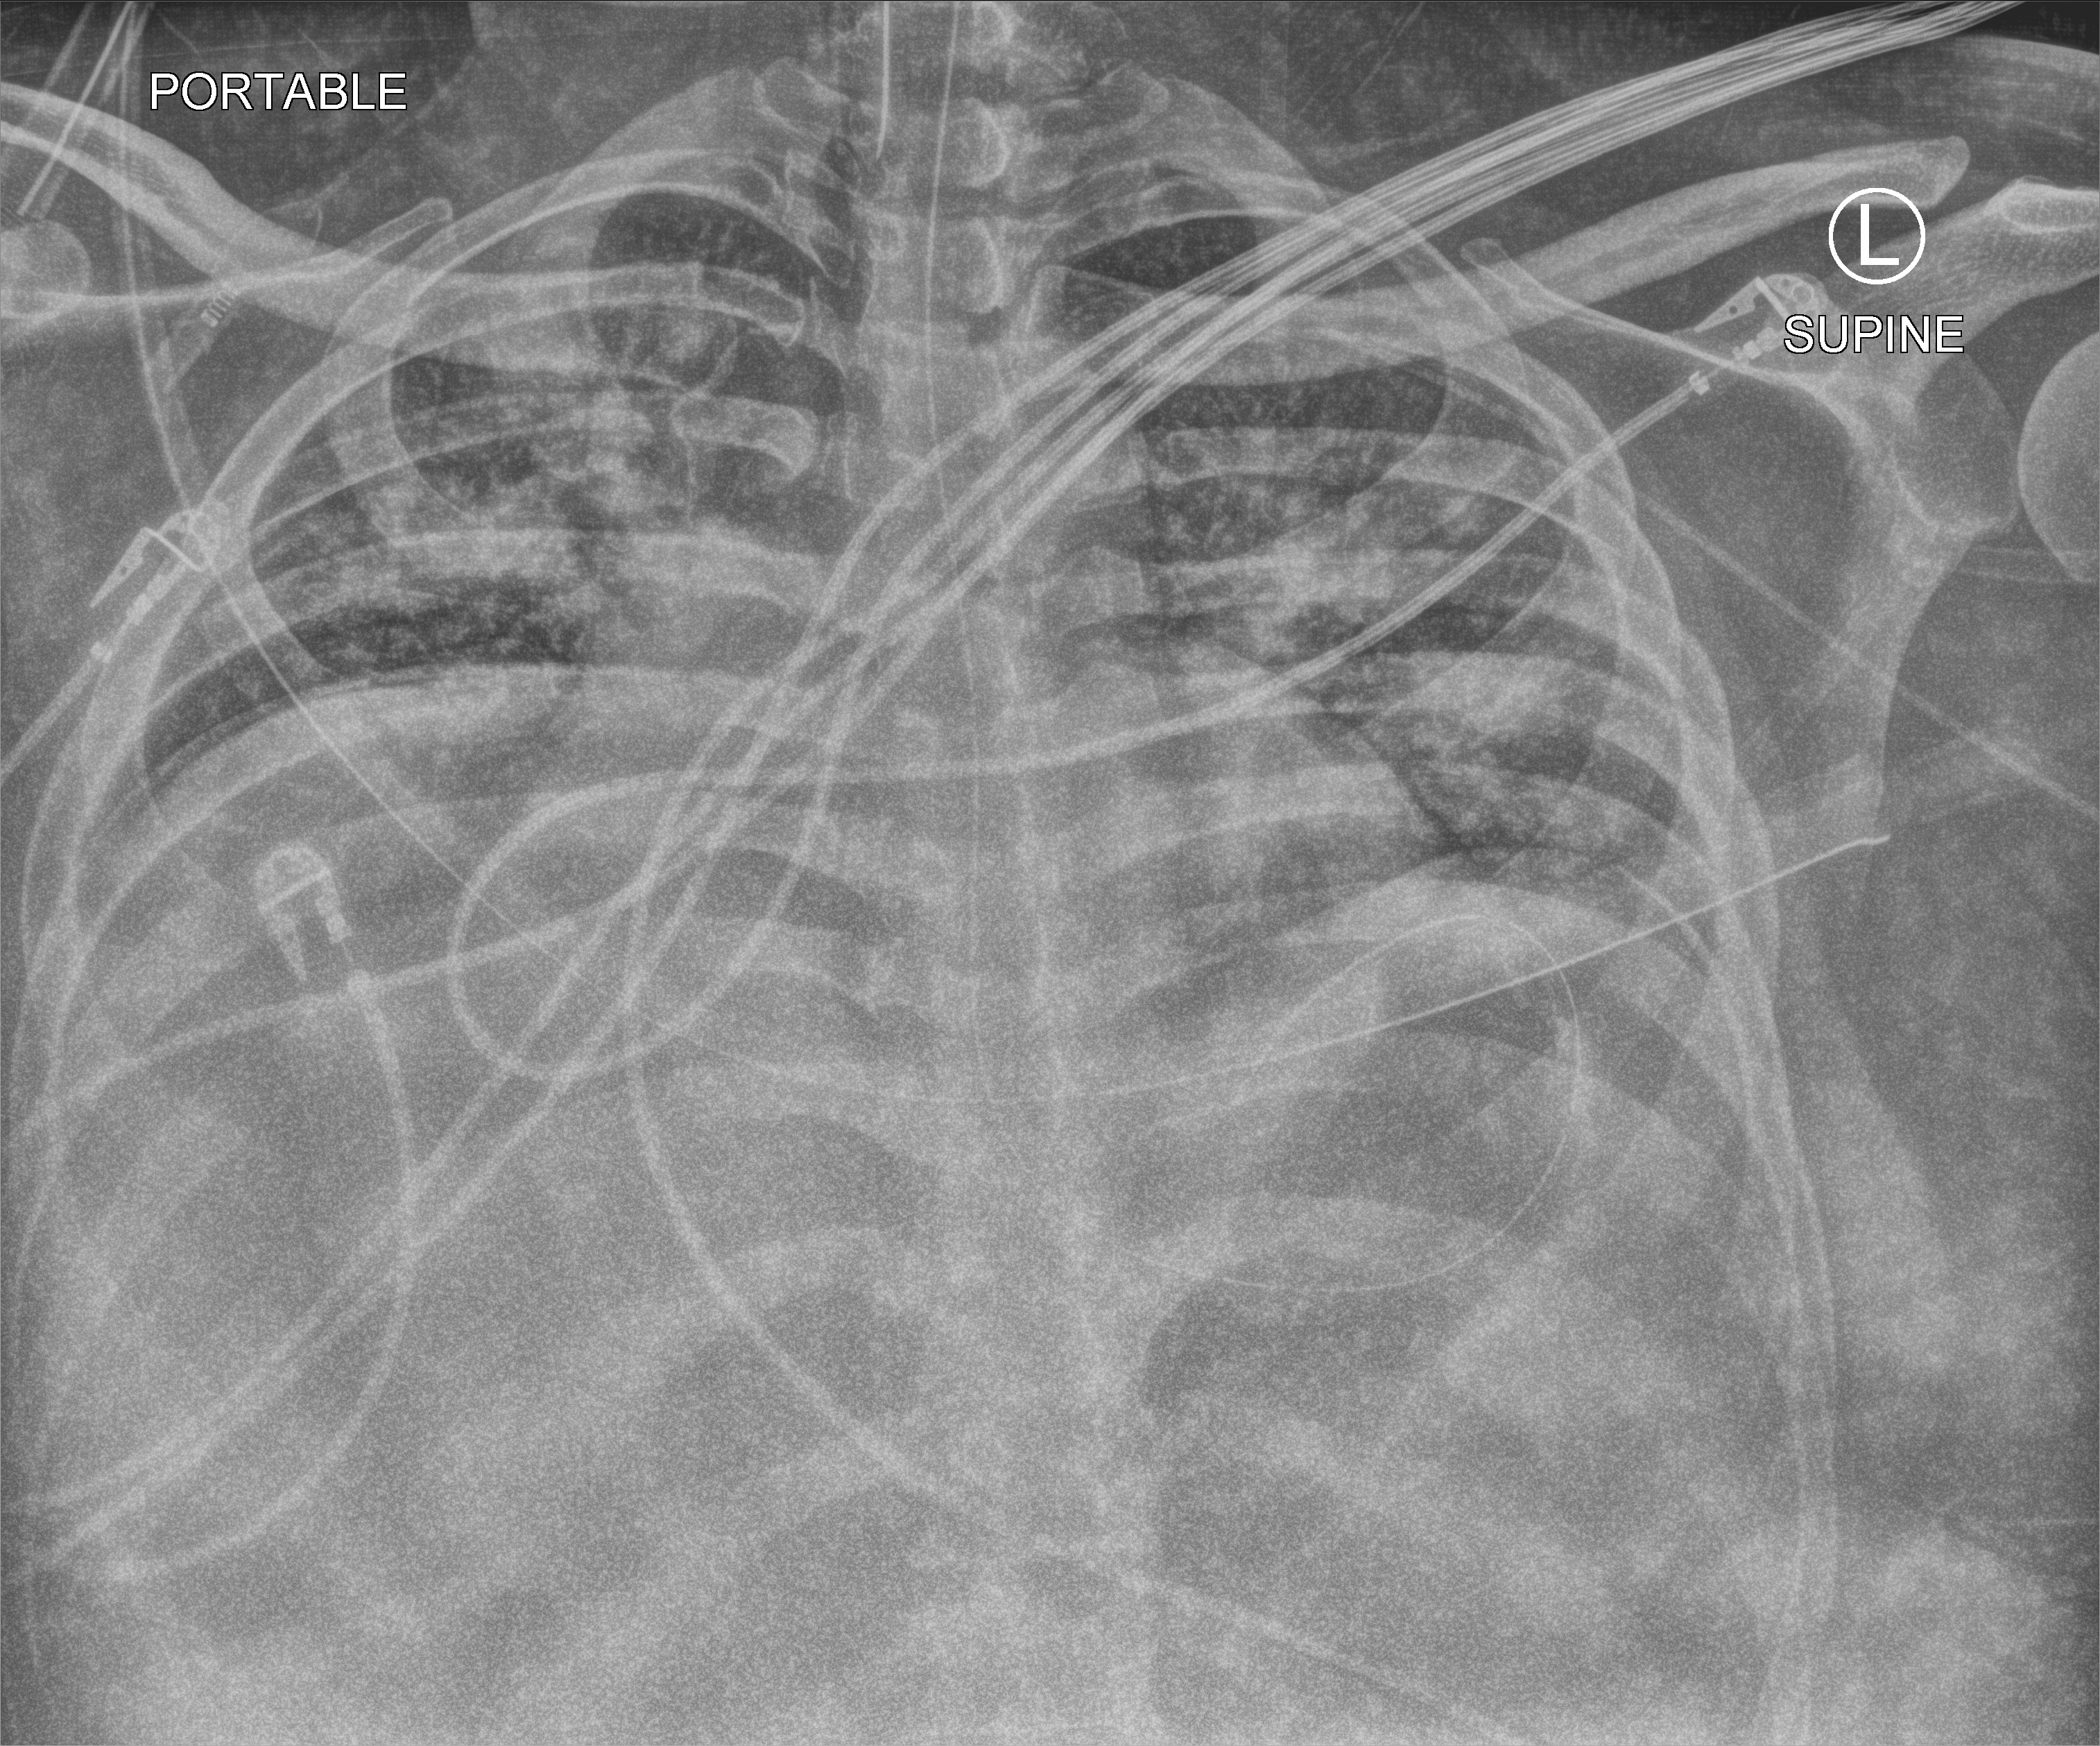
Bedside chest radiograph (computed radiography). Male patient hospitalised with COVID-19, age 18–59 years.
Hospital-stay facts (about this admission, not read from this image; timing relative to this image not recorded):
- other chronic lung disease (admission record): yes
- admitted to intensive care during this hospital stay: yes
- hypertension (admission record): no